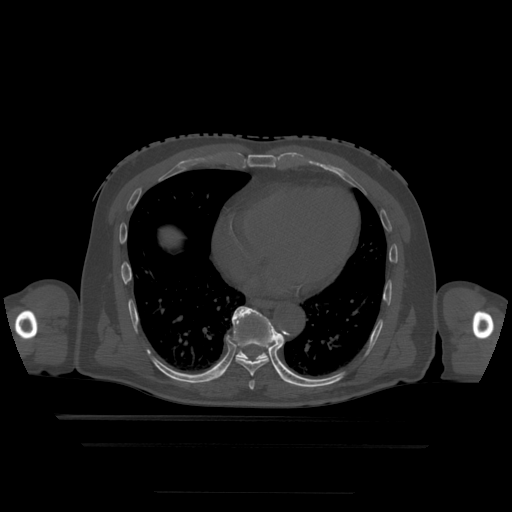
CT including the spine, one axial slice; slice 274 of 522 in the series (ordered by position); bone window (W 1800 / L 400 HU); 1.25 mm slice thickness; 512 × 512 image matrix. Patient age 68 years. From the clinical record (not read from this slice): primary cancer: urothelial.
Annotated regions visible in this slice (semi-automatic segmentation, software-assisted and operator-edited):
- T7 vertebra: bounding box <249,381,255,390> (left, top, right, bottom; pixels)
- T8 vertebra: <234,307,277,377>
- T9 vertebra: <225,307,280,375>